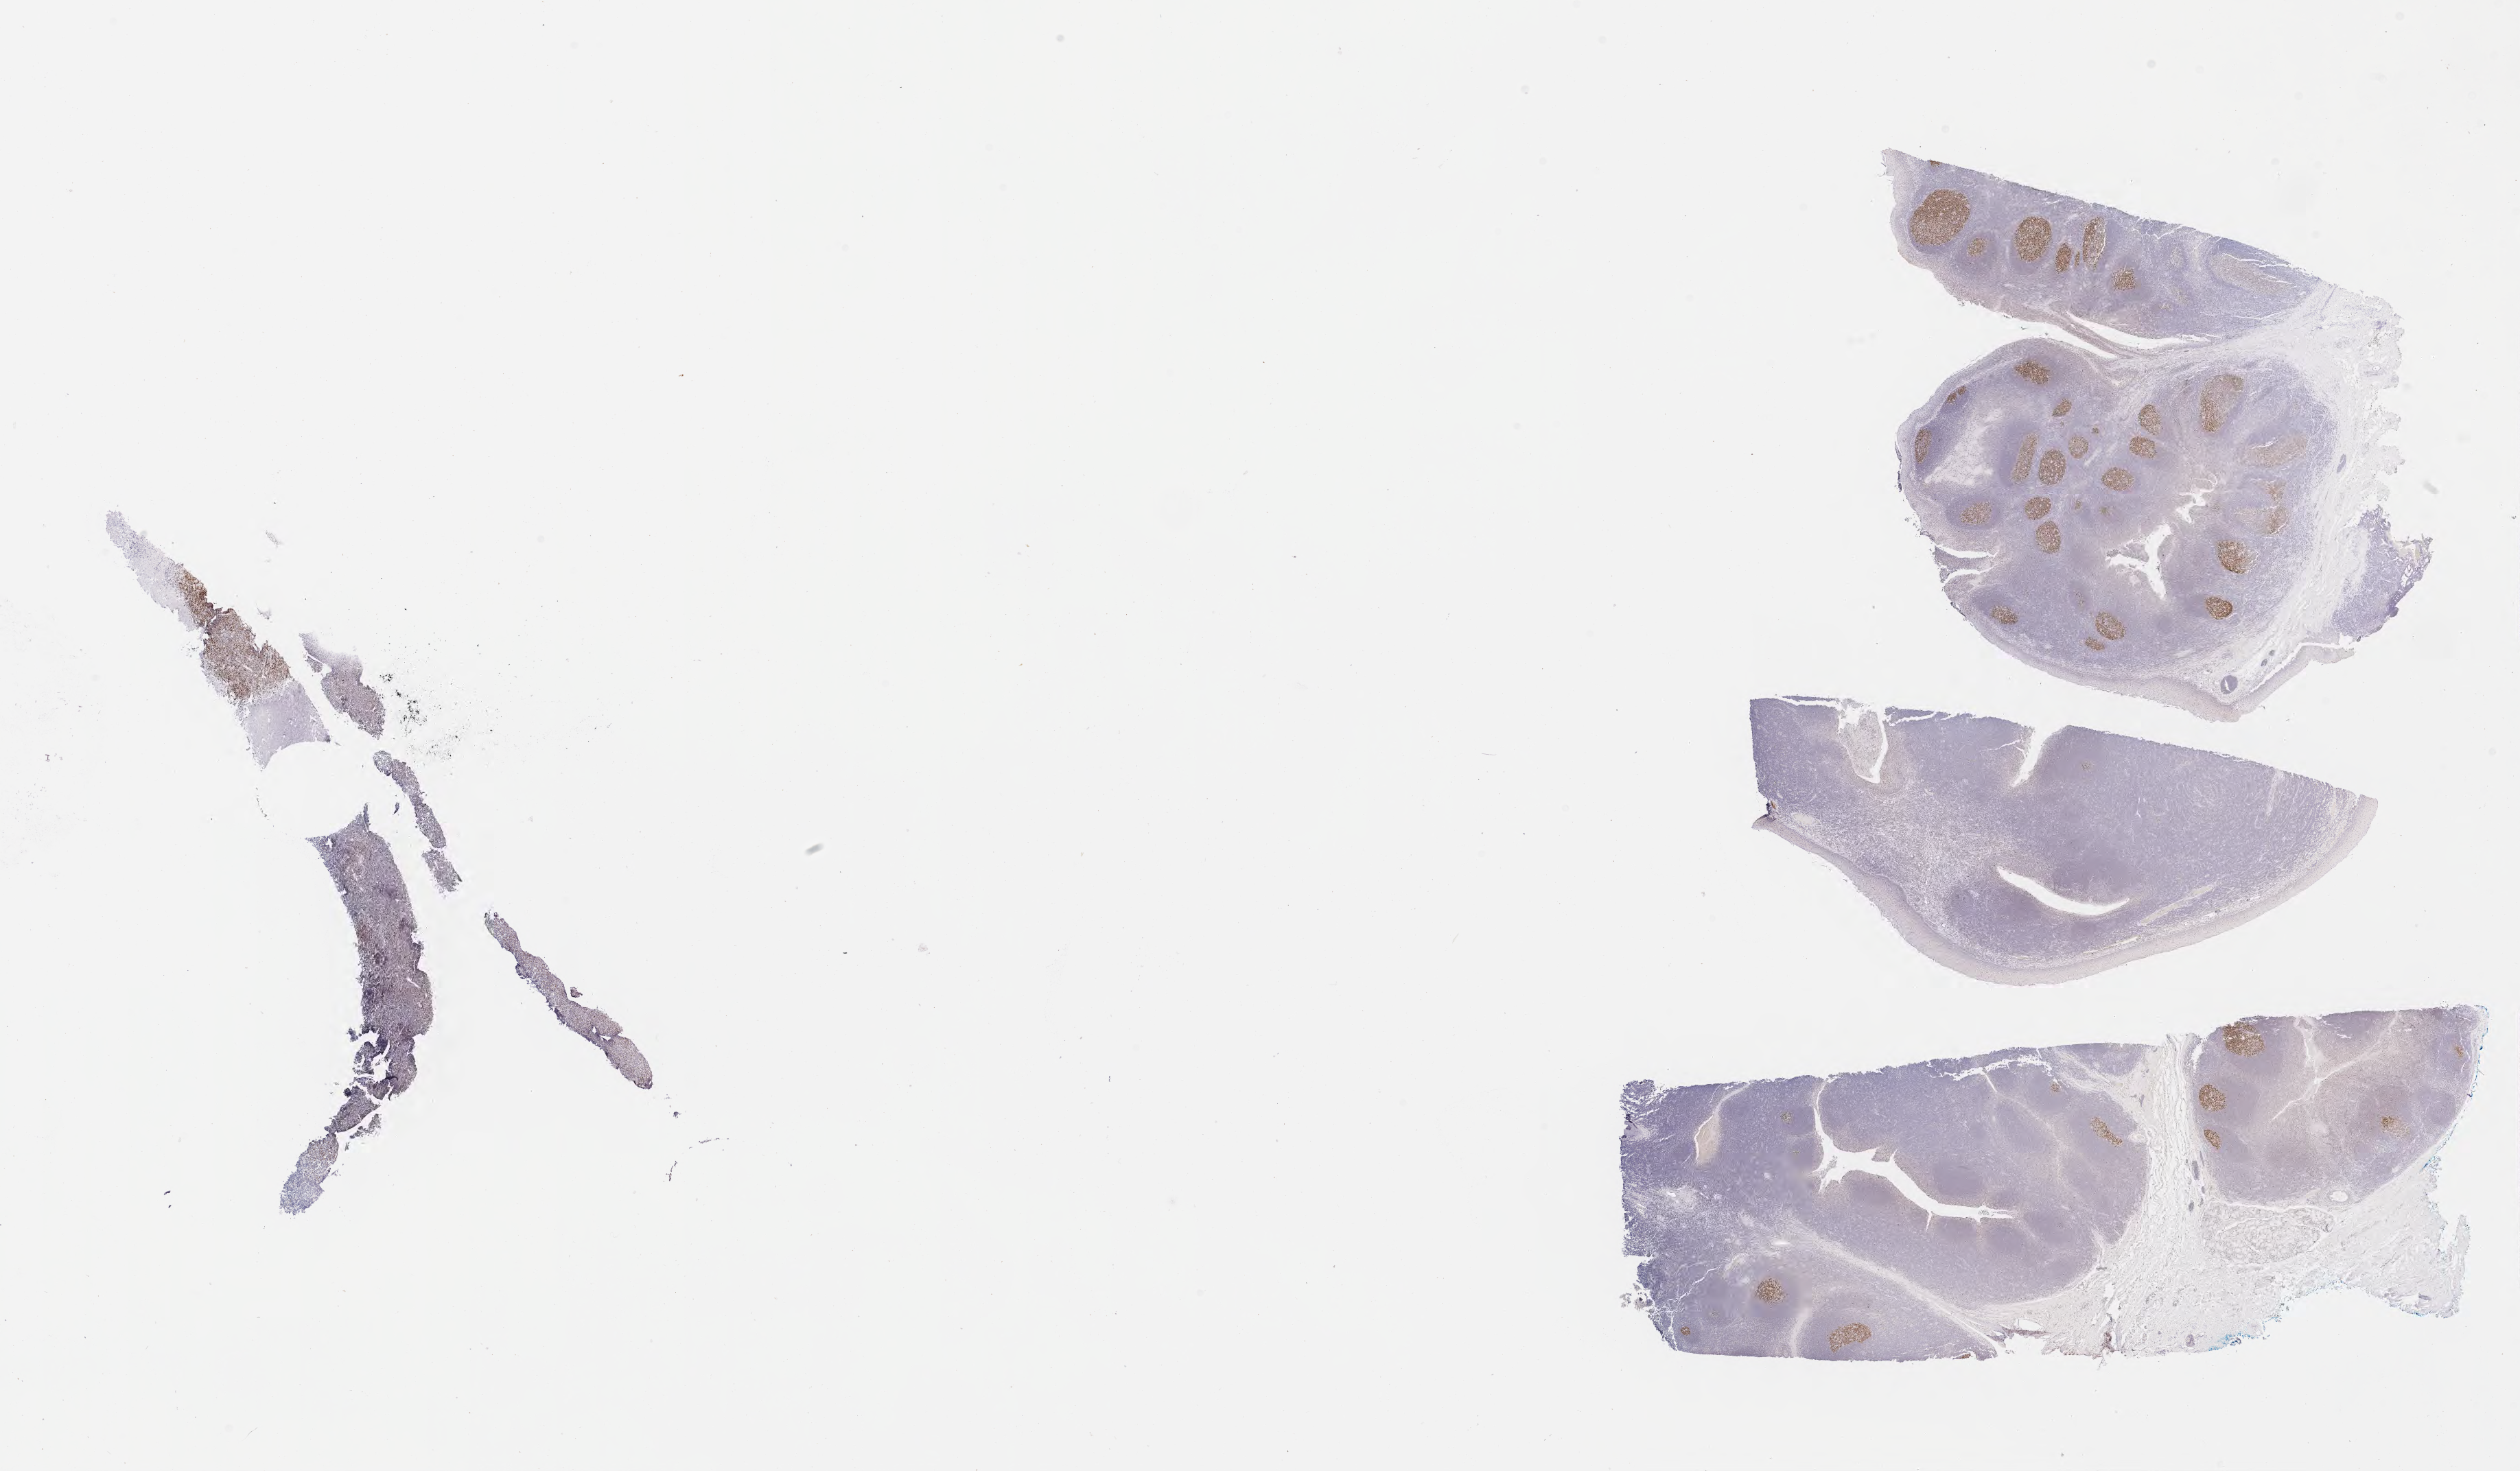
Immunohistochemistry (IHC) whole-slide image stained for BCL6 — low-resolution overview of the scanned area, about 29.7 x 17.3 mm, tumor tissue, site: abdomen proper. Patient: male, aged 14.
Diagnosis: Burkitt lymphoma, NOS.